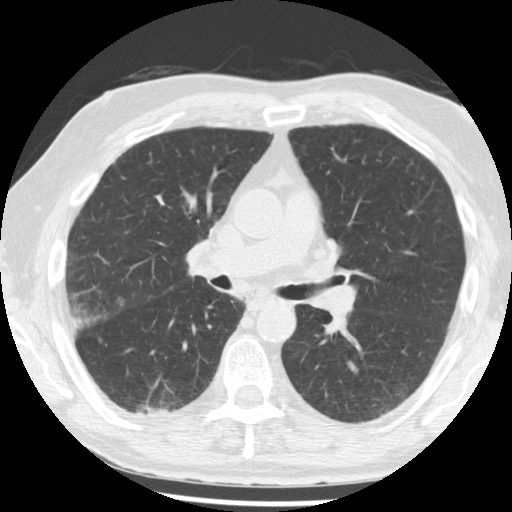
Low-dose screening chest CT, one axial slice. Position 119 of 221 along the scan axis. Reconstruction kernel STANDARD. 120 kVp. Lung window (W 1500 / L -600 HU). 512 × 512 image matrix, field of view 350 × 350 mm.
Structures marked on this image (expert manual segmentation):
- lesion 1 (tumor, lower lobe of right lung): bounding box (x1, y1, x2, y2) in pixels: (140, 405, 172, 416)